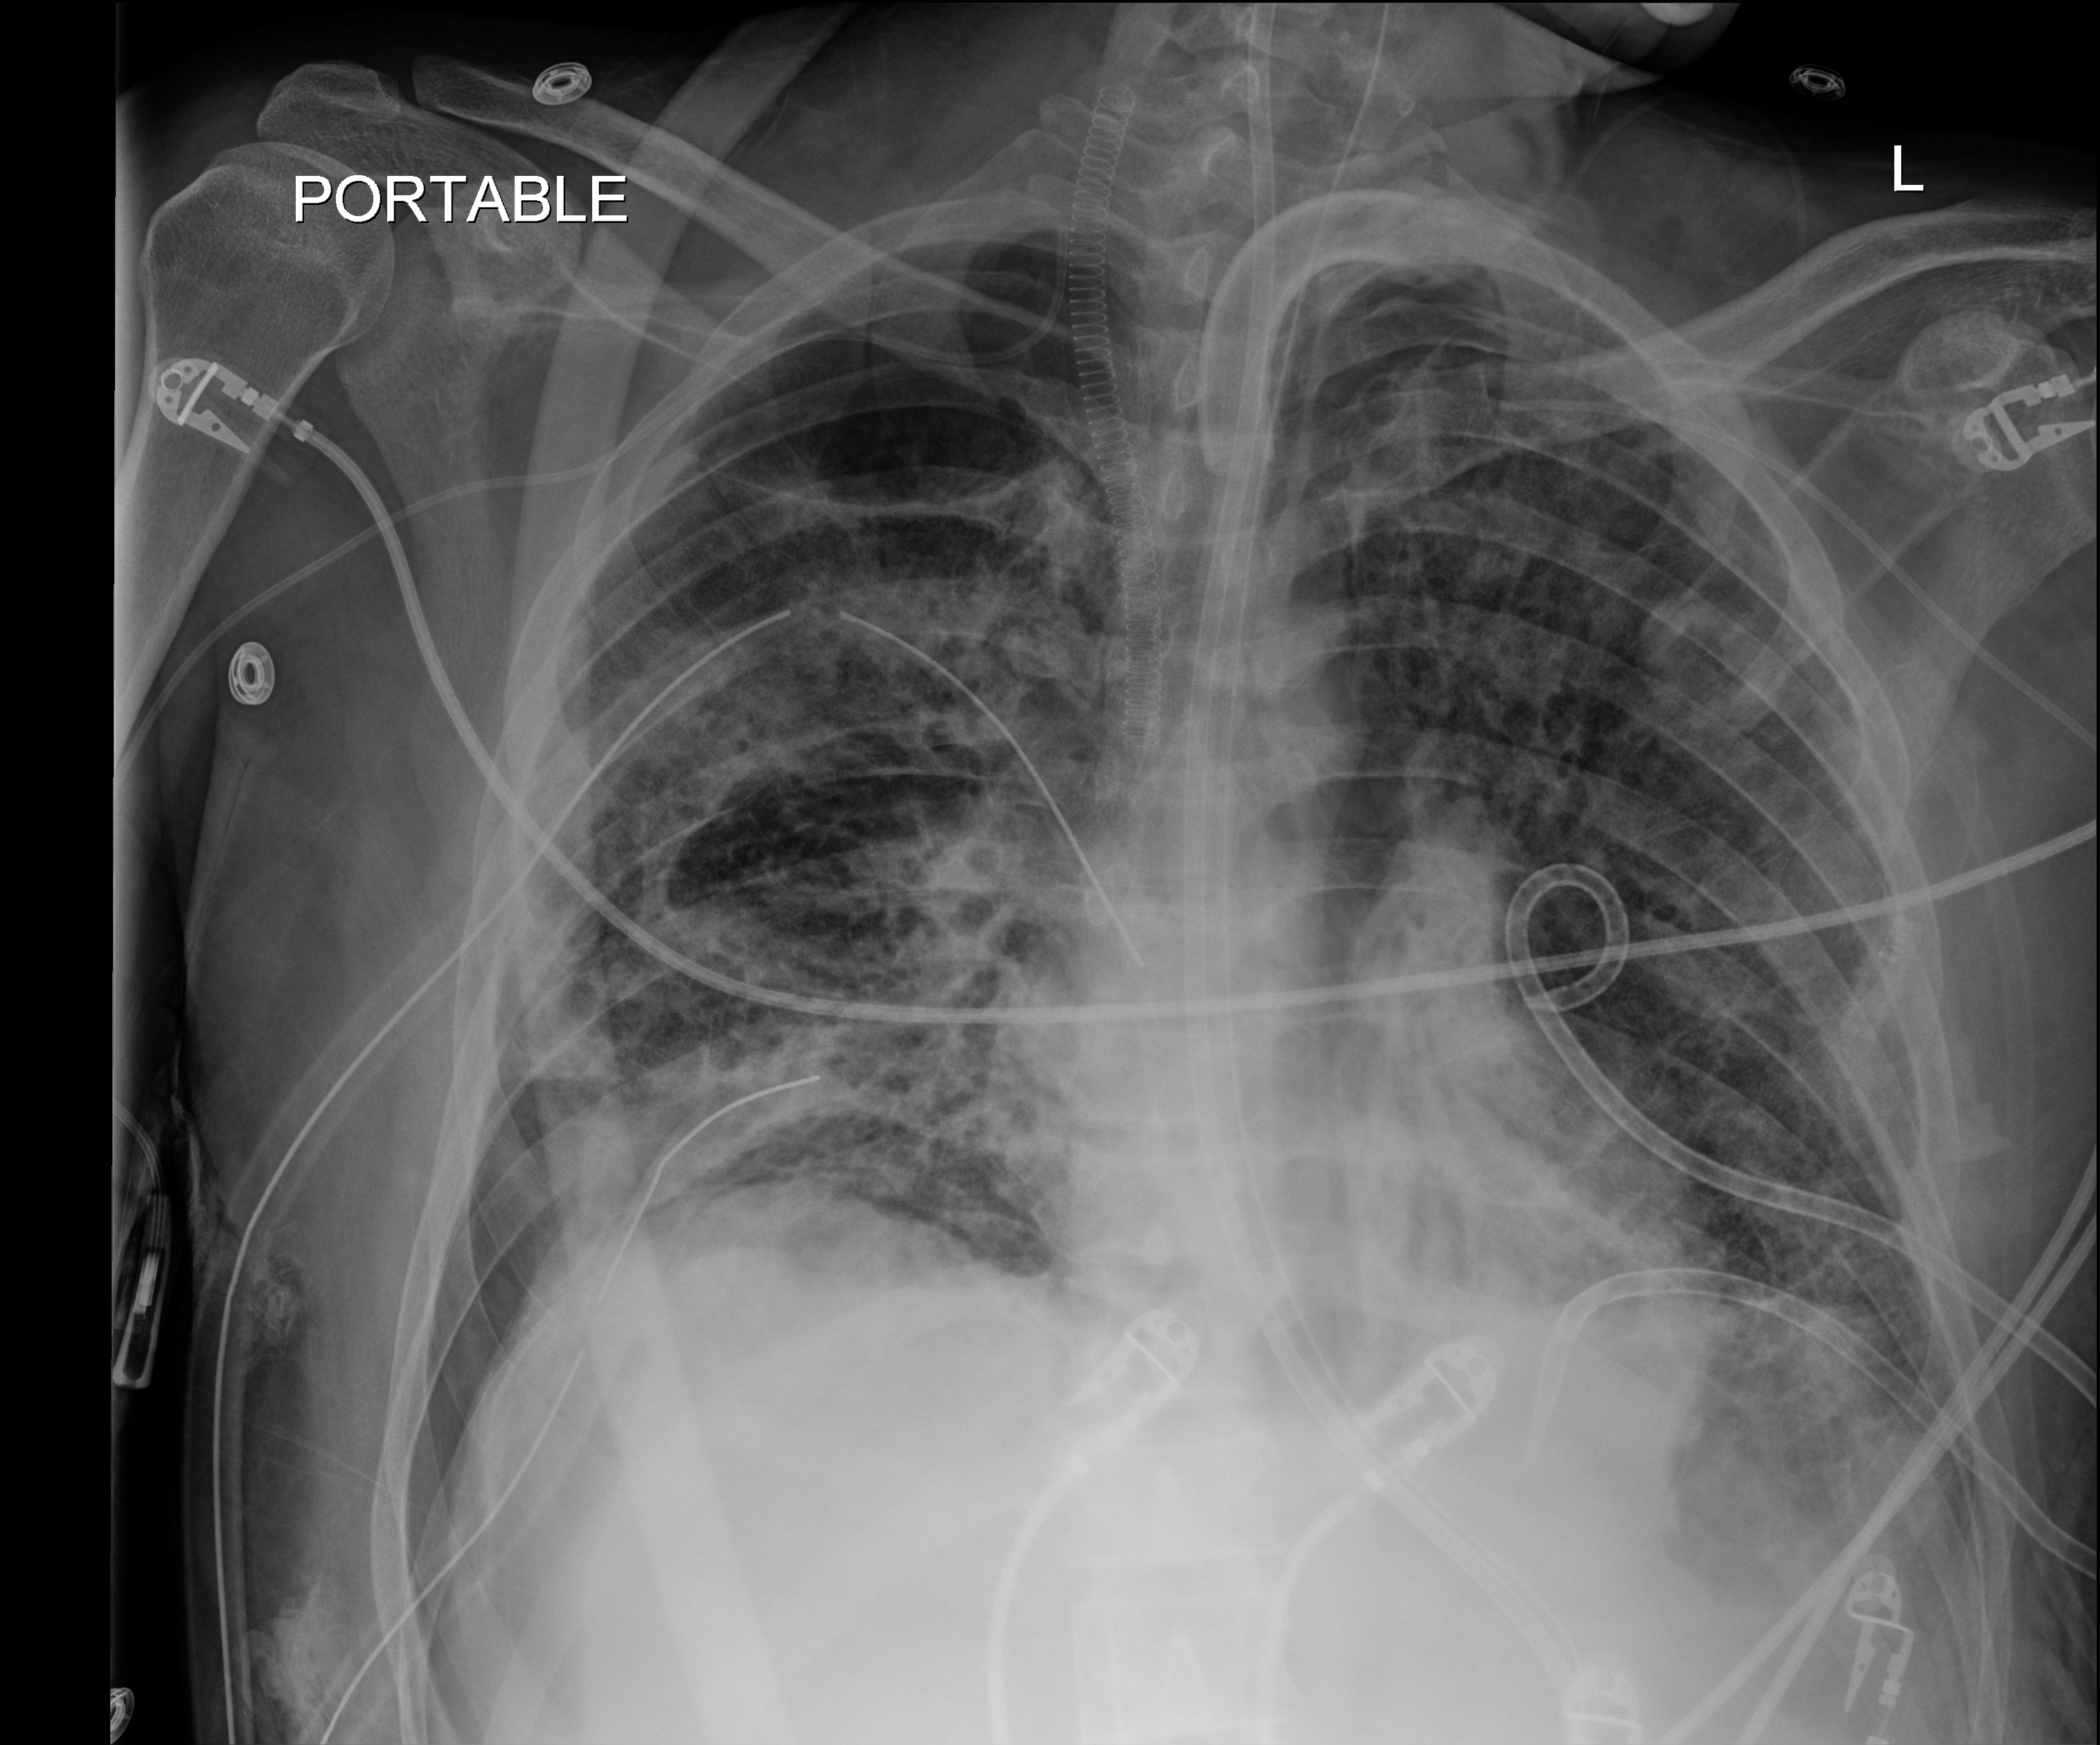
Bedside chest radiograph (digital radiography); anteroposterior (AP) projection. Adult patient hospitalised with COVID-19, age 18–59 years.
Admission-level facts for this patient (not findings on this image; timing relative to this image not recorded): chronic kidney disease (admission record): no; admitted to intensive care during this hospital stay: yes.